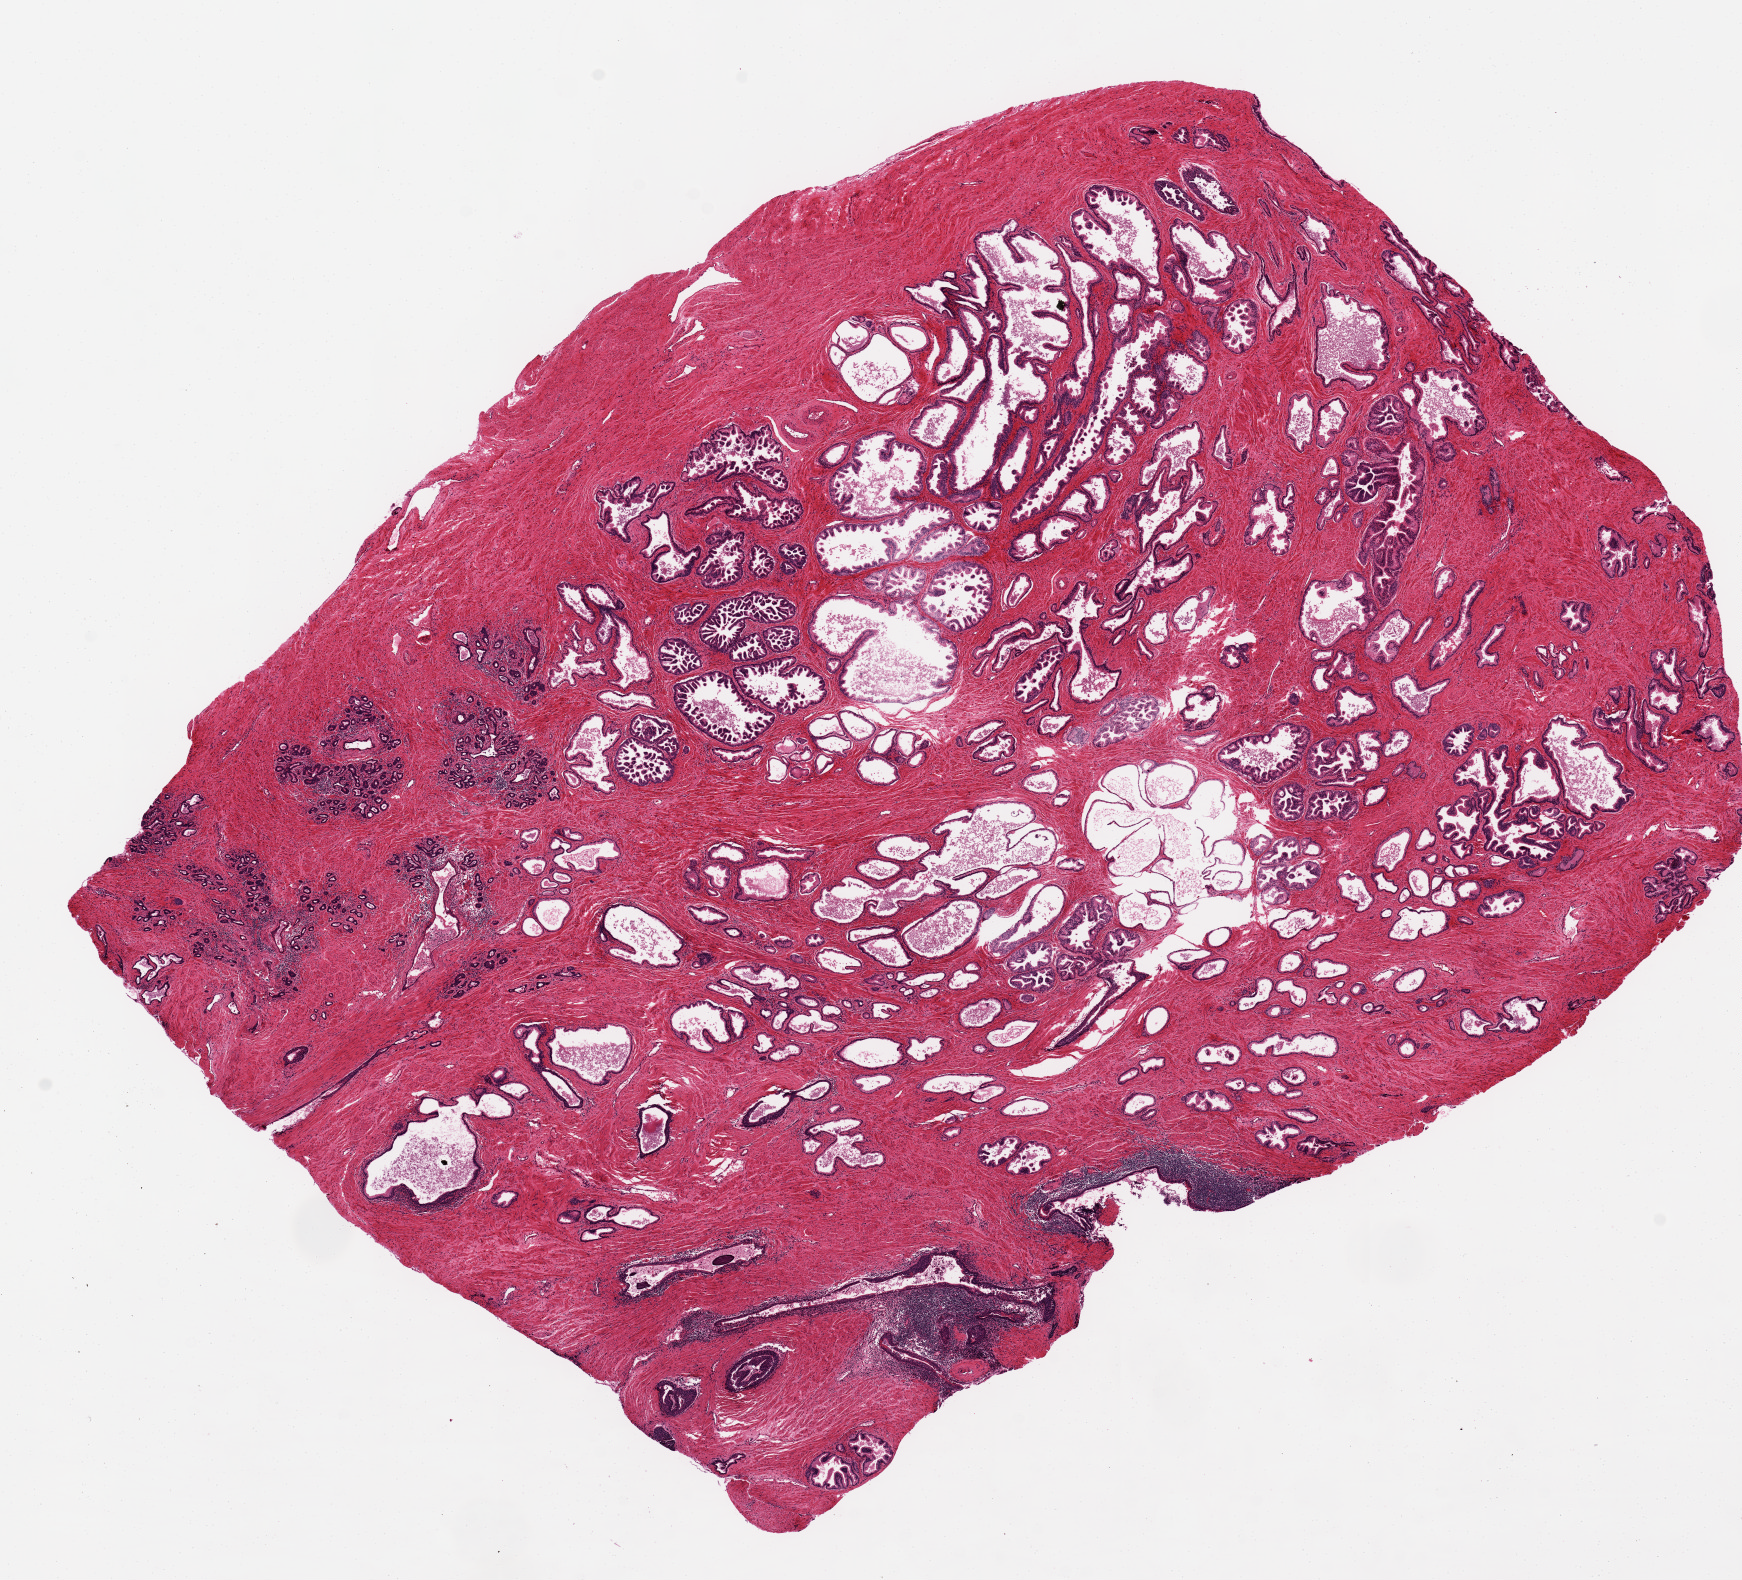
Whole-slide image, H&E stain, brightfield, a low-resolution overview of the entire scanned area, about 13.8 x 12.5 mm (acquisition: 20x scan). PAXgene-fixed, paraffin-embedded tissue. Section of prostate (target tissue). Tissue donor sample. Male donor.
Pathologist's review note for this sample: 13 x 9.7mm. Remarkably well preserved. Patchy glandular (papillary) hyperplasia, focal chronic prostatitis.